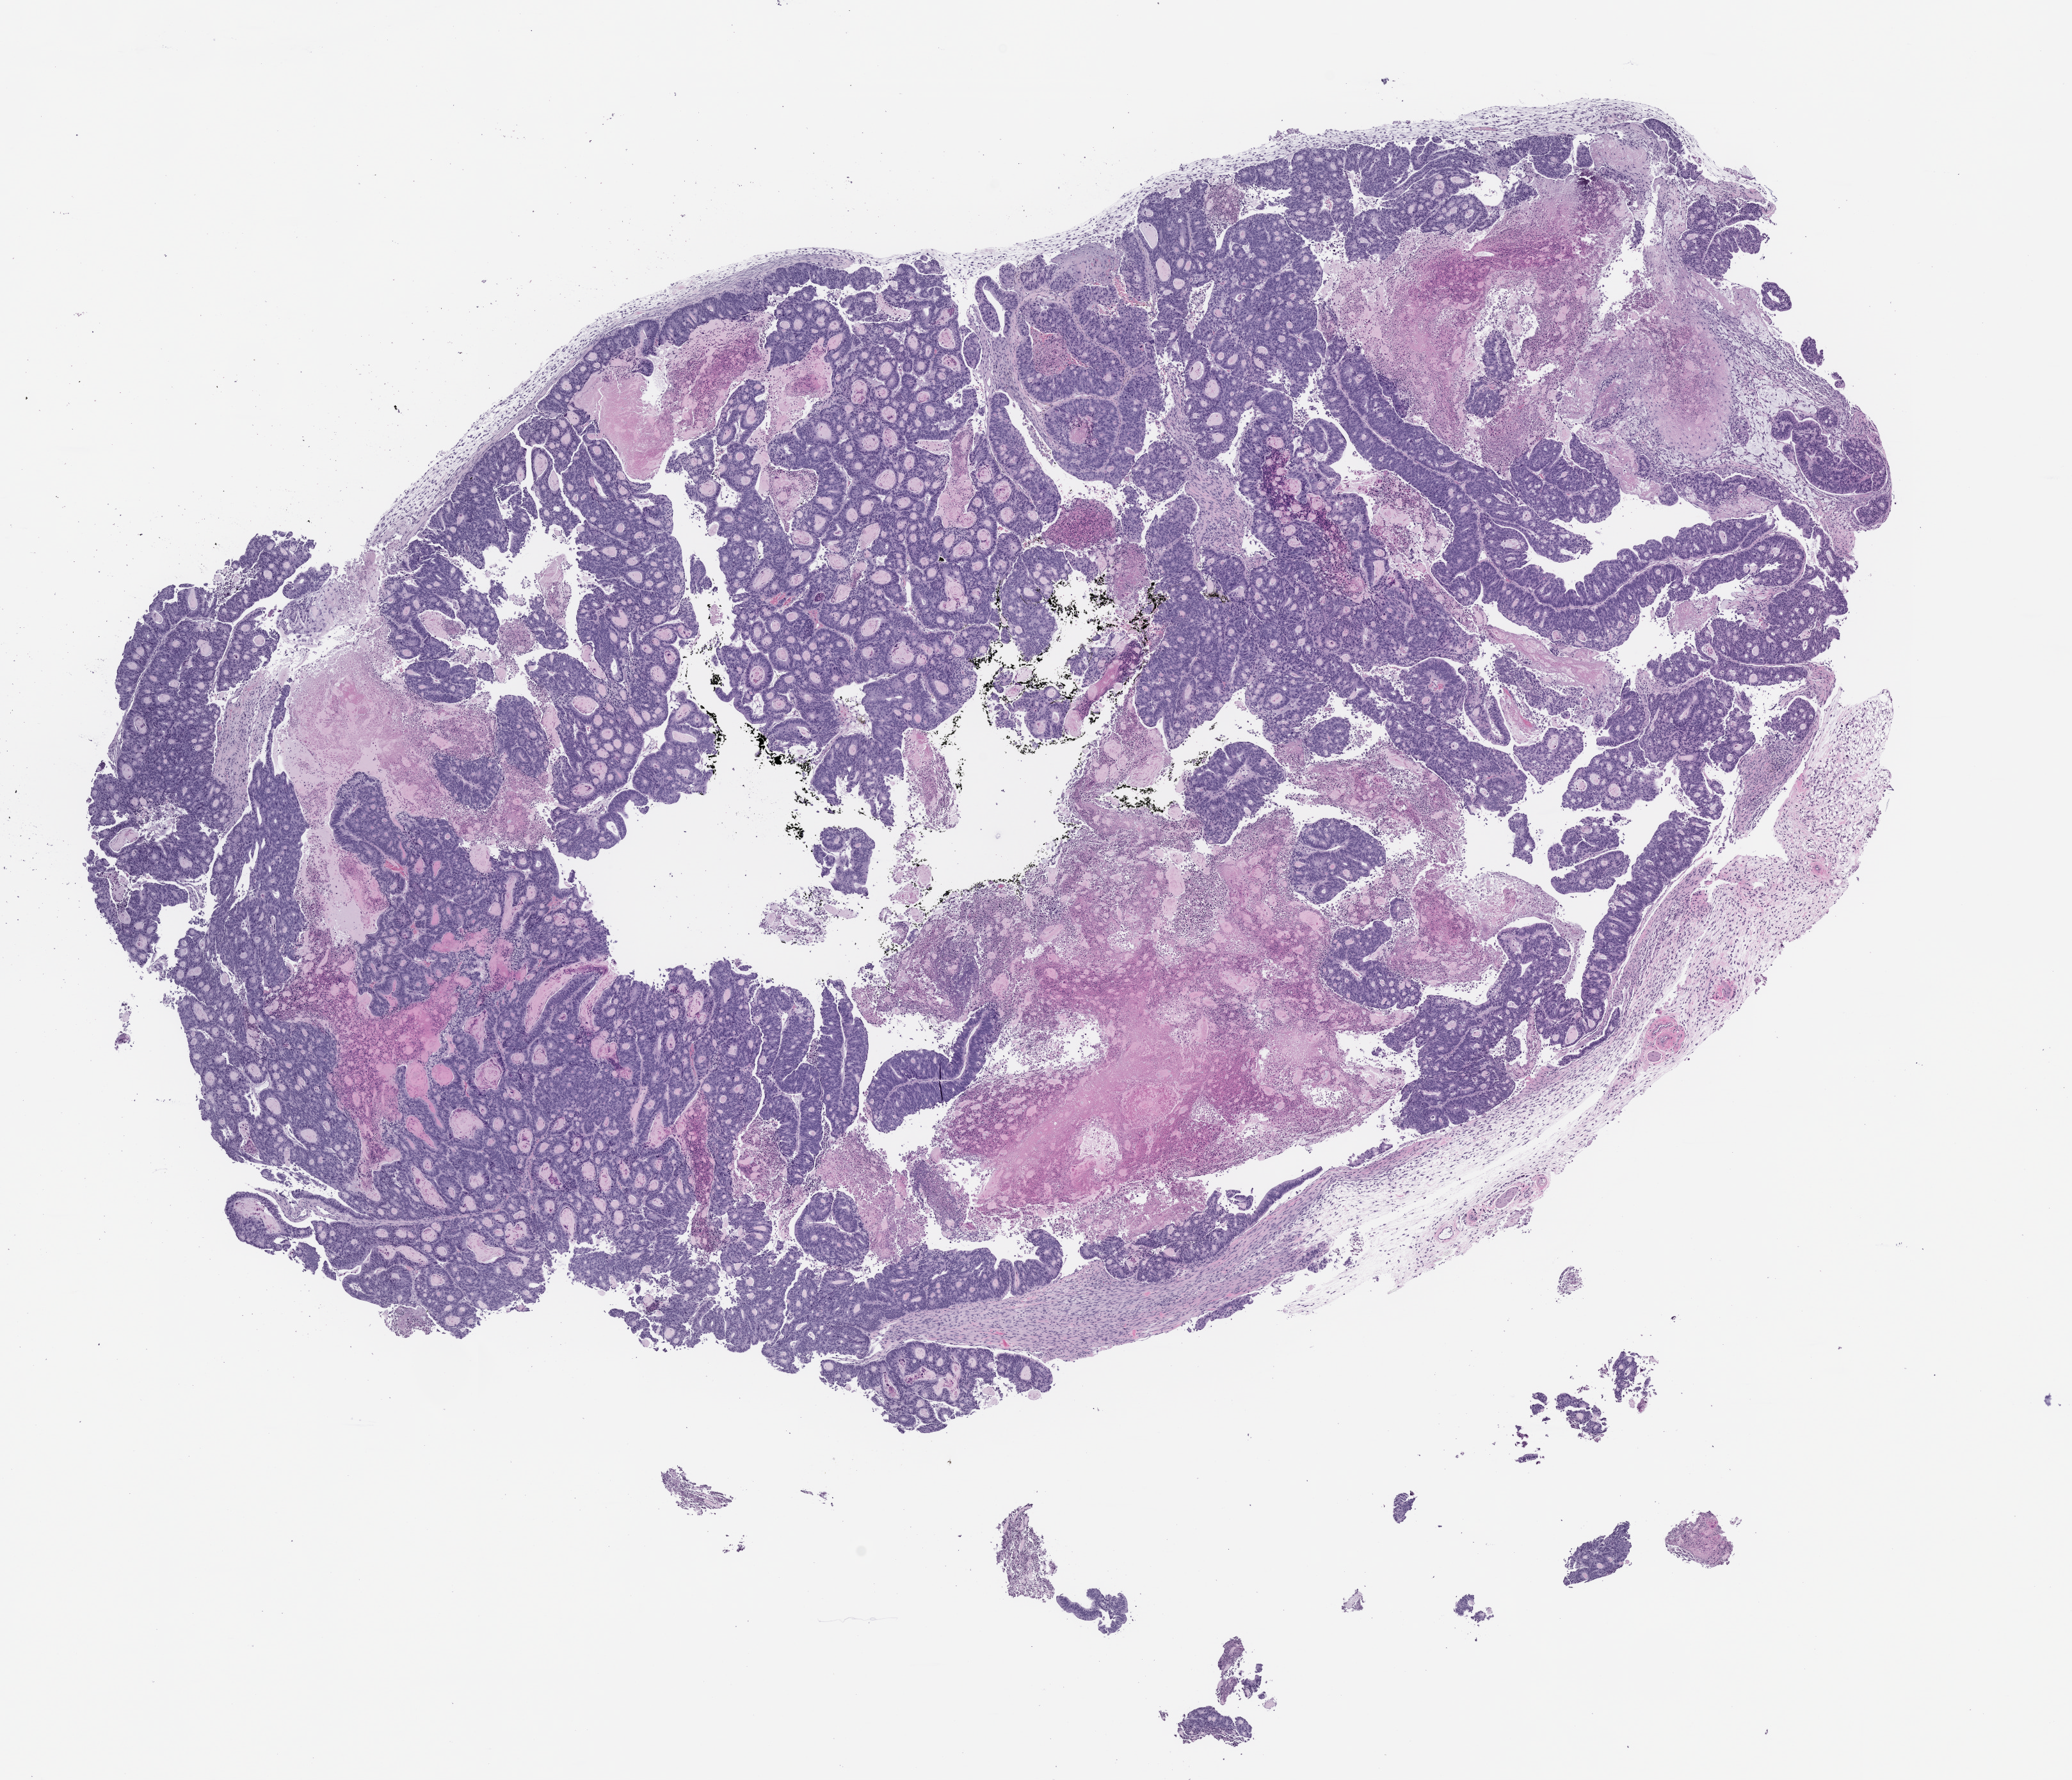
Hematoxylin and eosin (H&E) whole-slide image of a patient-derived xenograft (PDX) tumor grown in a mouse, passage 1, a low-resolution overview of the entire scanned area, about 13.0 x 11.2 mm, formalin-fixed paraffin-embedded section, tumor site category: colon.
• originating patient diagnosis: Colon Adenocarcinoma